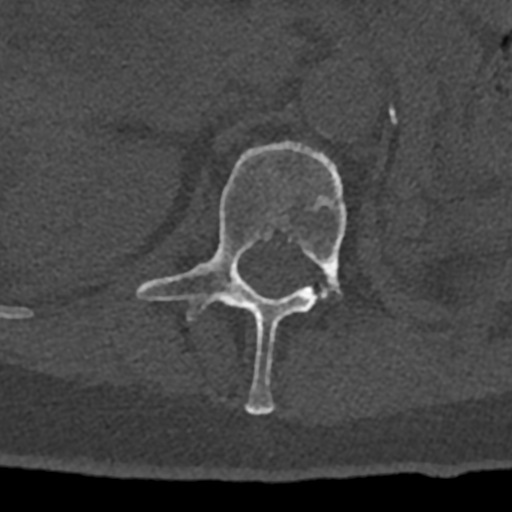
CT including the spine, one axial slice. Slice 433 of 797 in the series (ordered by position). 120 kVp. Bone window (W 1800 / L 400 HU). 0.5 mm slice thickness. 512 × 512 image matrix, field of view 160 × 160 mm. Male patient, age 74 years. From the clinical record (not read from this slice): primary cancer: renal; vertebrae with lytic lesions (as recorded): T10, L1, L2, L3, L4, L5.
Outlined on this slice (semi-automatic segmentation, software-assisted and operator-edited):
- L1 vertebra: box from (x=136, y=141) to (x=347, y=415) px